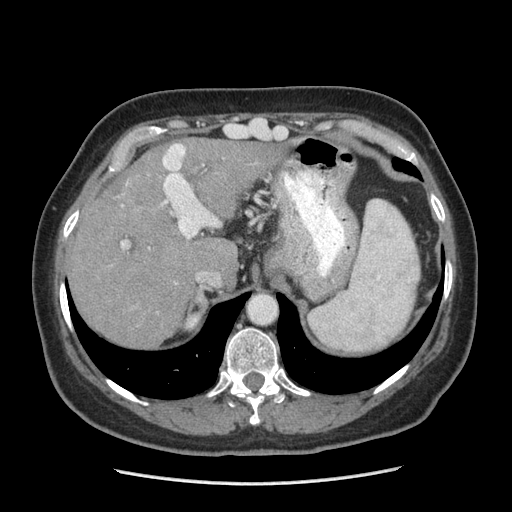
Contrast-enhanced abdominal CT (liver protocol), one axial slice; position 160 of 185 along the scan axis; 140 kVp; soft-tissue window (W 400 / L 40 HU); 2.5 mm slice thickness; 512 × 512 image matrix, field of view 360 × 360 mm. Case-level facts recorded for this patient, not image findings: diagnosis: hepatocellular carcinoma (patient treated with transarterial chemoembolisation; whether this scan precedes or follows treatment is not stated here); TNM stage (as recorded): Stage-I; Child-Pugh class: A; tumour differentiation: poorly differentiated.
Outlined on this slice (semi-automatic segmentation, software-assisted and operator-edited):
- abdominal aorta: box from (x=249, y=296) to (x=275, y=323) px
- liver parenchyma outside the tumour (the mass and vessels are separate outlines, so this box may not span the whole liver): (x=66, y=137)–(x=282, y=346)
- mass: (x=119, y=165)–(x=166, y=224)
- liver vessels: (x=121, y=144)–(x=219, y=248)